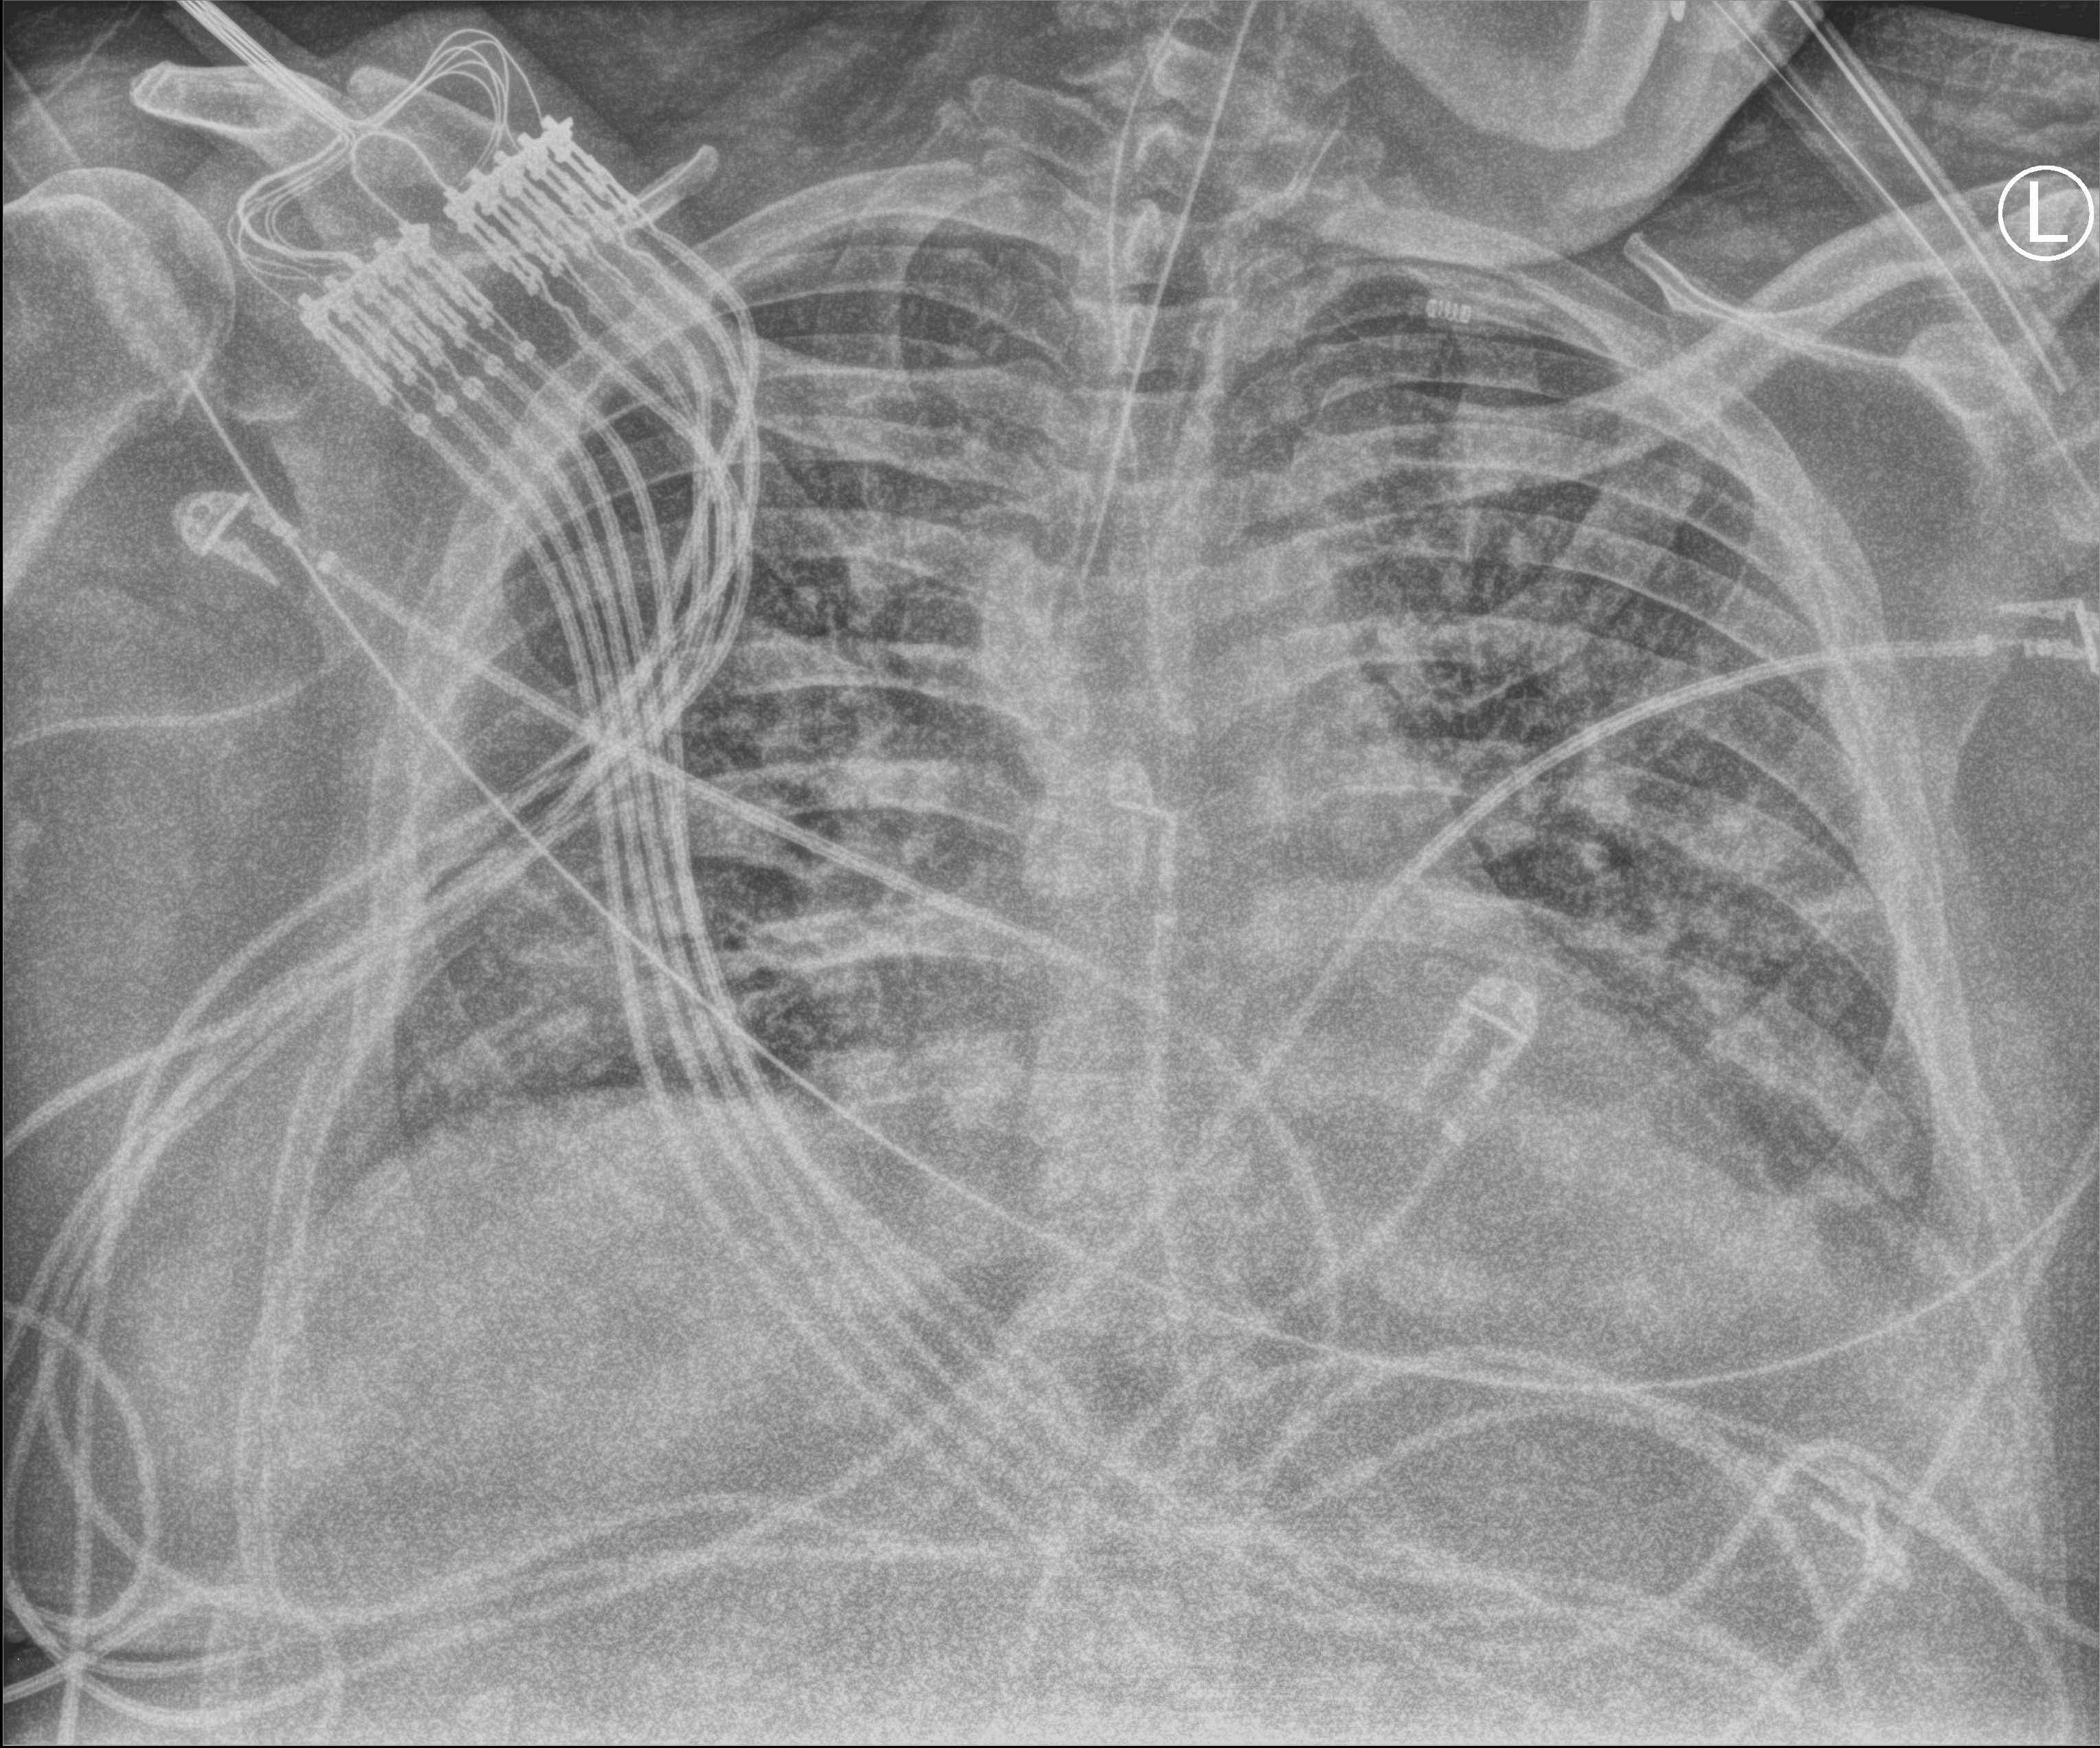
Bedside chest radiograph (computed radiography); anteroposterior (AP) projection. Male patient hospitalised with COVID-19, age 60–74 years.
Hospital-stay facts (about this admission, not read from this image; timing relative to this image not recorded): COPD (admission record): no.